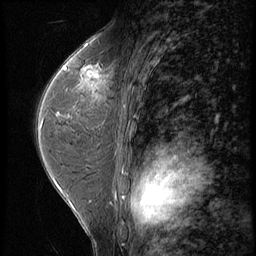
Breast MRI (dynamic contrast-enhanced), one sagittal slice; position 35 of 56 along the scan axis; 3 images stored at this slice position (order not interpretable as contrast timing); 1.5 T; TE 4.2 ms, TR 9 ms; 256 × 256 image matrix, field of view 180 × 180 mm. Female patient, age 44 years. Case-level facts recorded for this patient, not image findings: setting: breast cancer imaged before/during neoadjuvant chemotherapy; receptor status: triple-negative.
Structures marked on this image (semi-automatically segmented with operator editing):
- analysis volume of interest (the breast-tissue region the enhancement analysis was run in; not a lesion): bounding box <71,54,112,99> (left, top, right, bottom; pixels)
- tumour enhancement mask (voxels above the 140 % enhancement threshold inside the analysis volume of interest): <83,67,104,78>